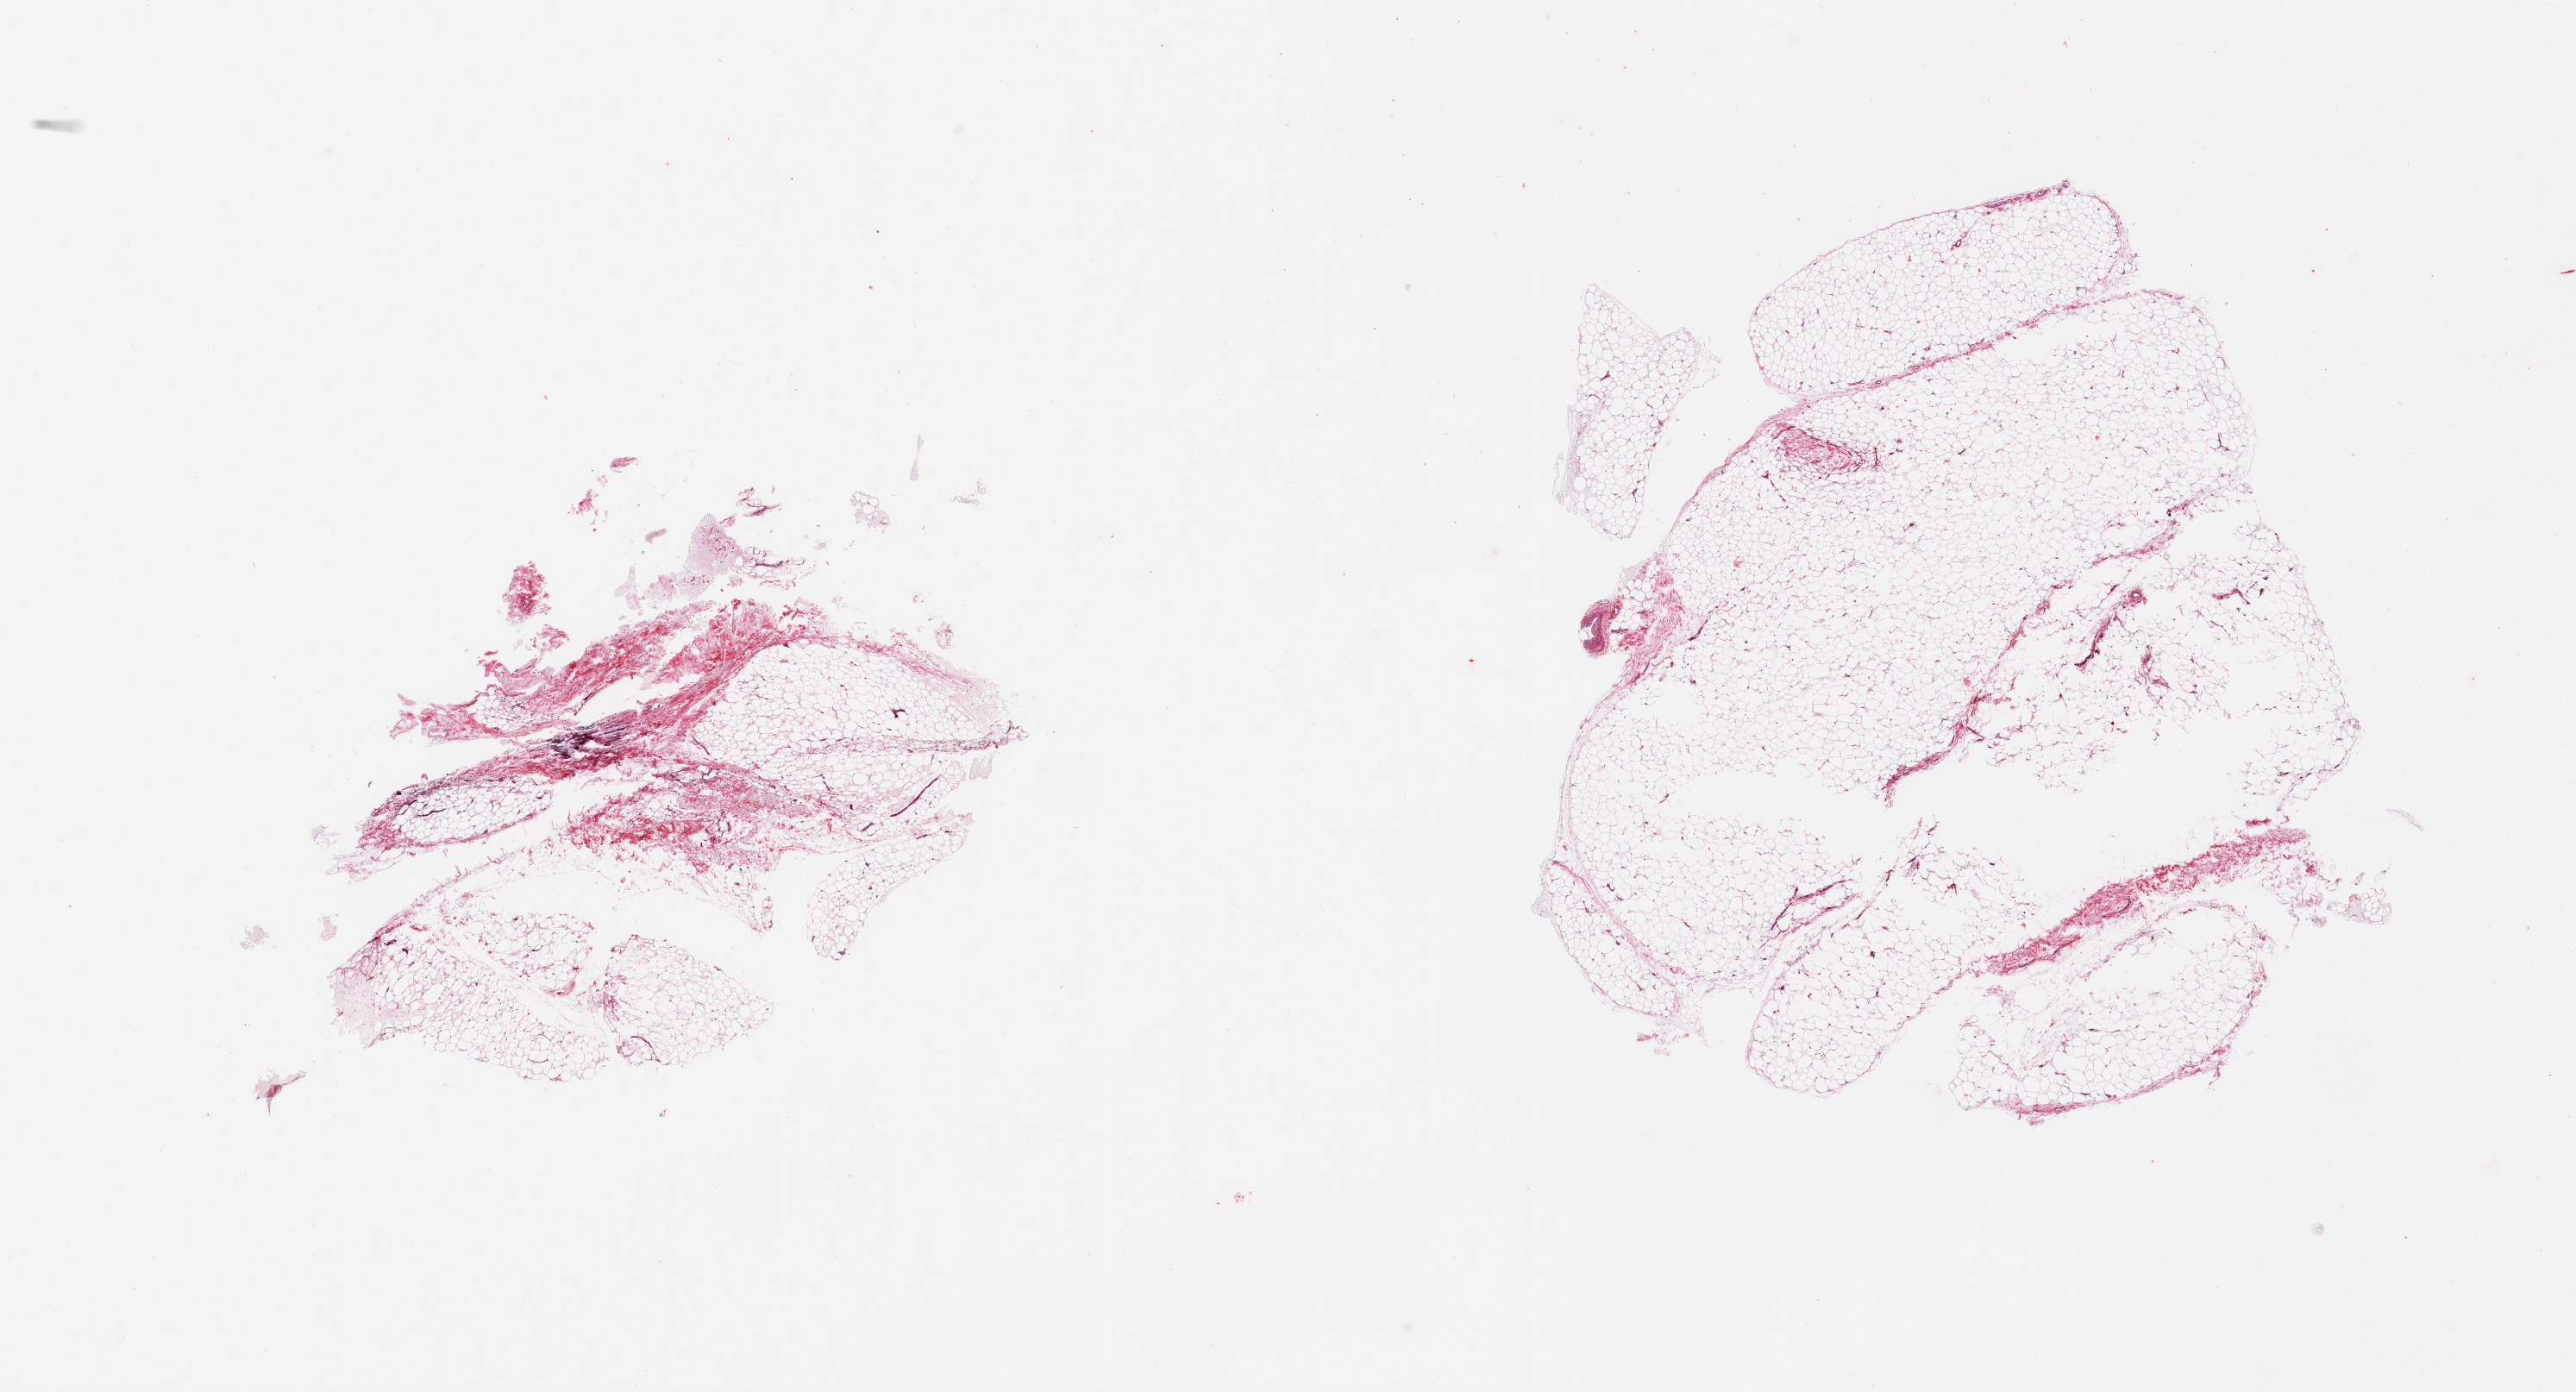
Whole-slide image, haematoxylin and eosin stain, brightfield, a low-resolution overview of the entire scanned area, about 23.6 x 12.8 mm. PAXgene-fixed paraffin-embedded (PFPE) section. Target tissue: adipose tissue. Donor tissue sample. Donor sex: male.
Review note (as recorded): 2 pieces, ~10% fascia.